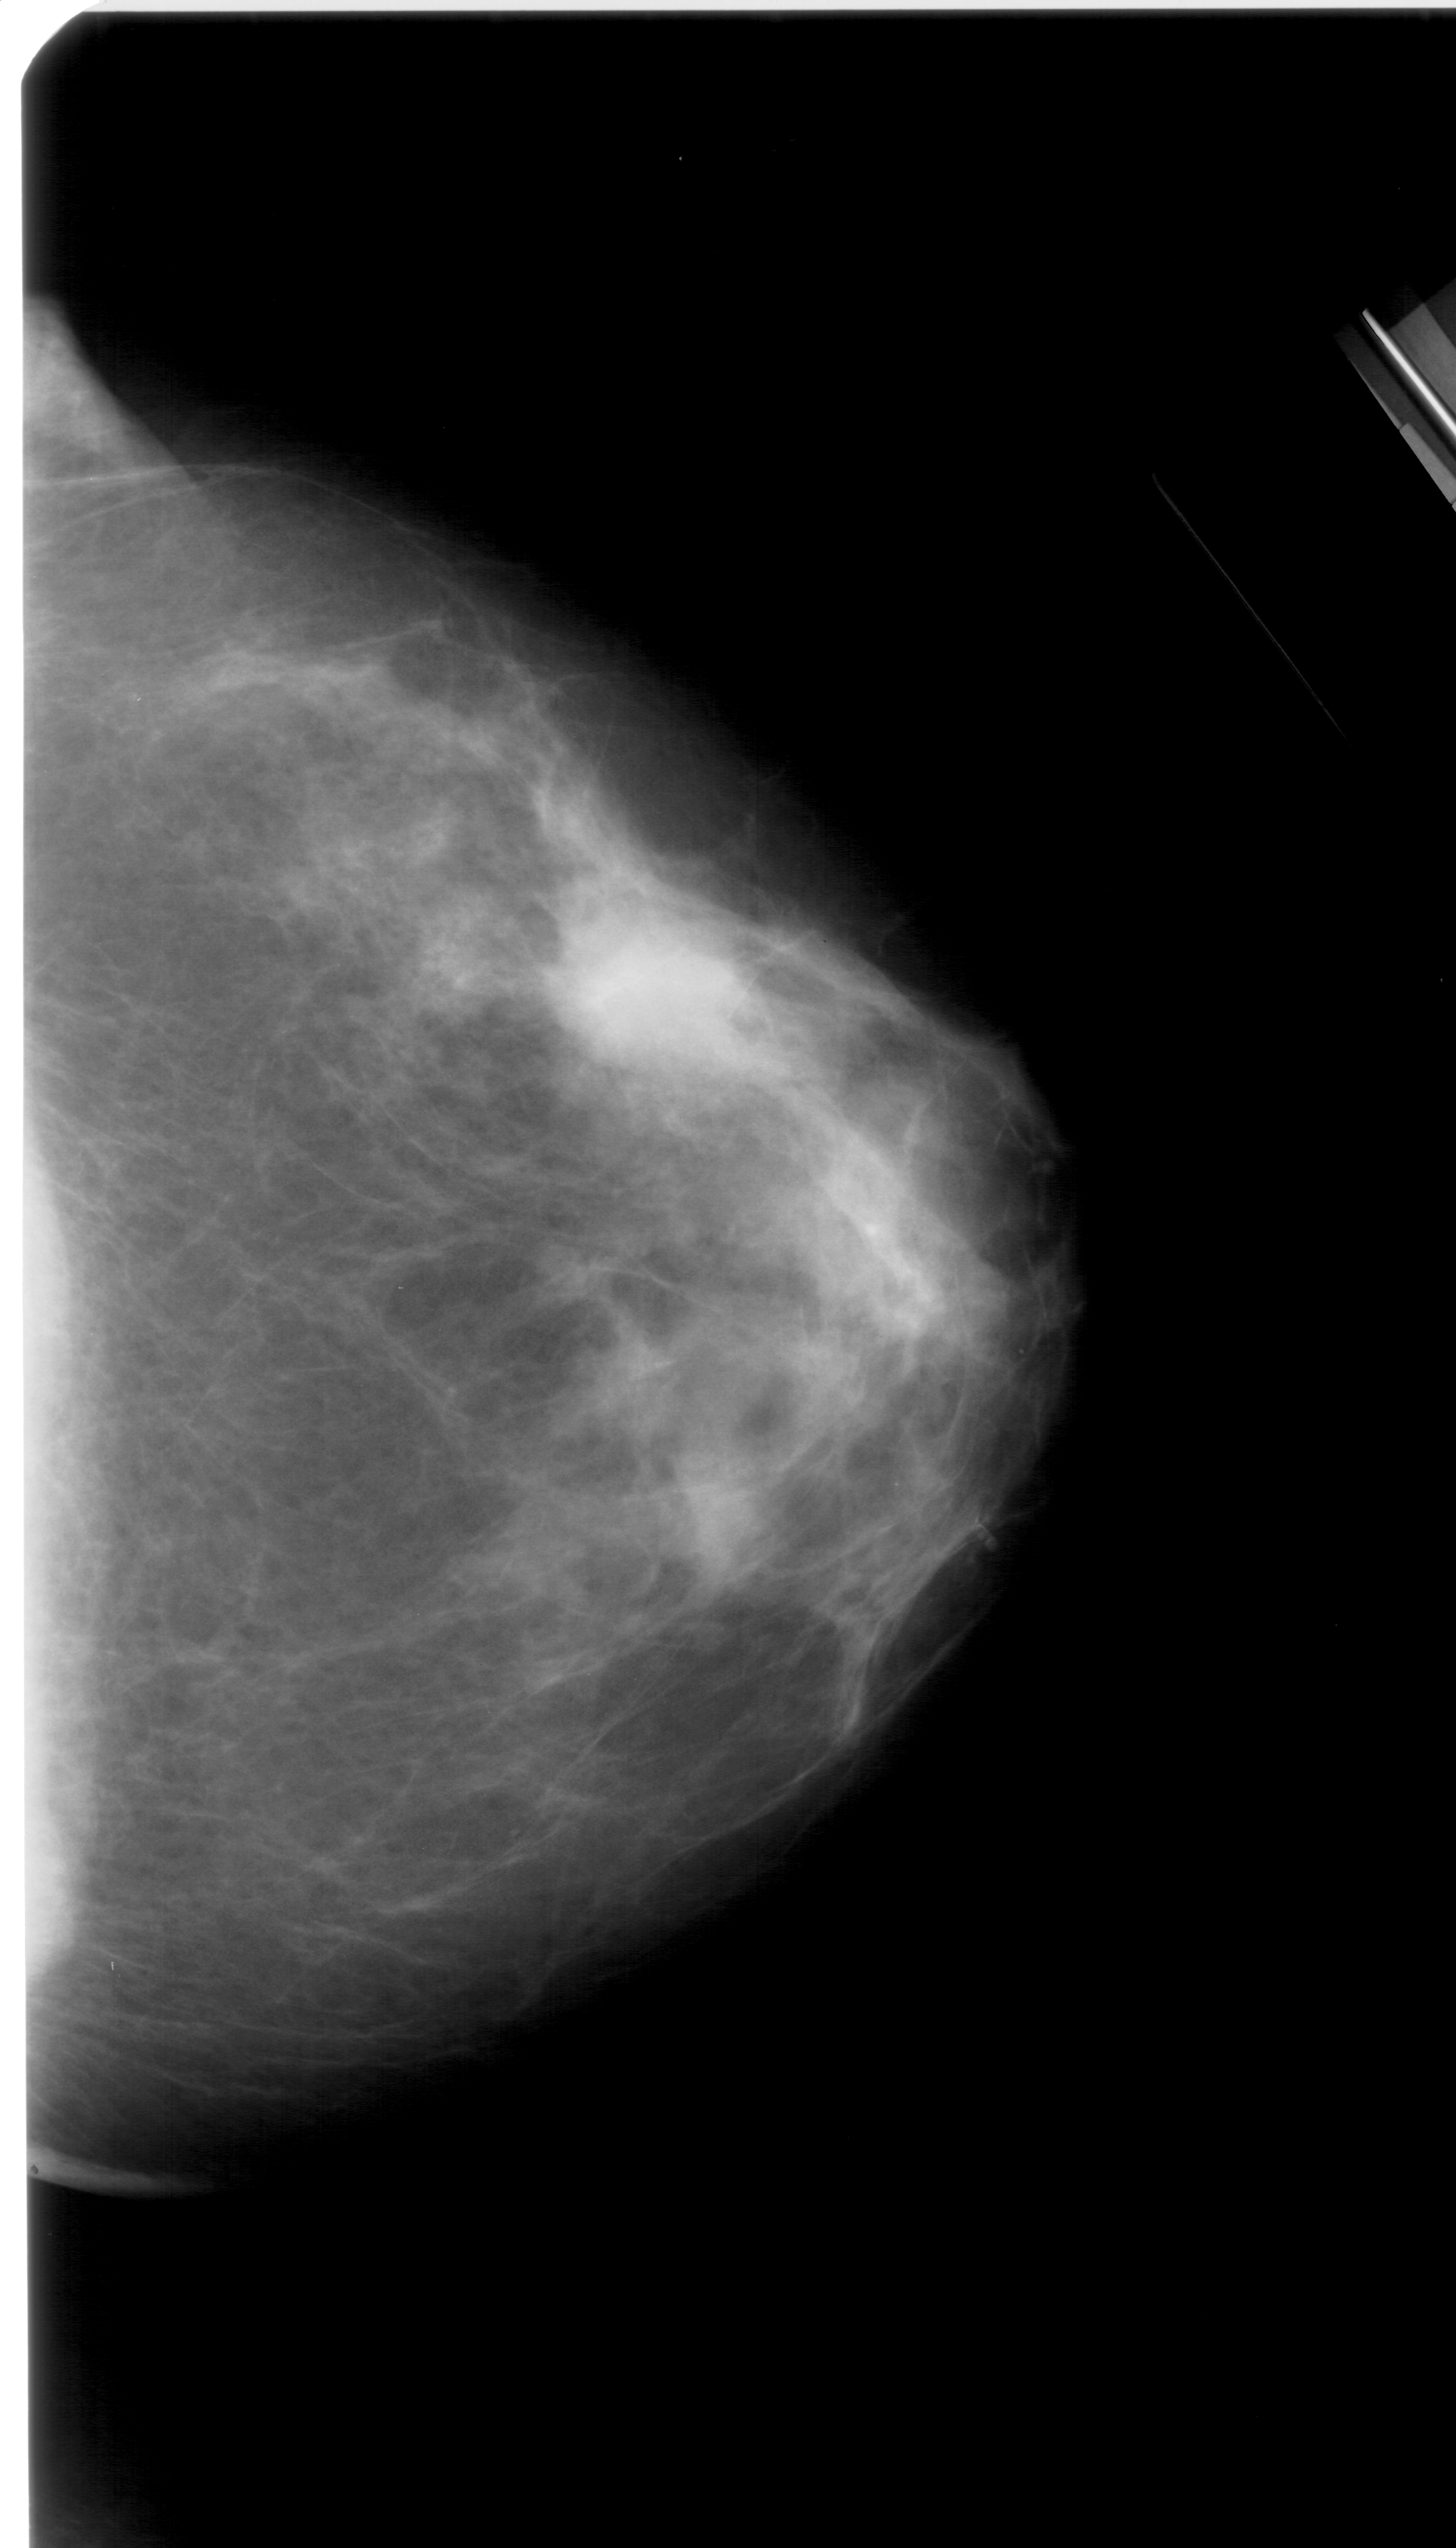
Scanned film-screen mammogram; right breast; craniocaudal (CC) view; breast composition: heterogeneously dense (BI-RADS density category 3 of 4).
- Abnormality record for this image: mass, shape irregular, margins ill defined; BI-RADS assessment category 4; subtlety rating 3 on a 1 (subtle) to 5 (obvious) scale; pathology result (as recorded, not read from the image): malignant.